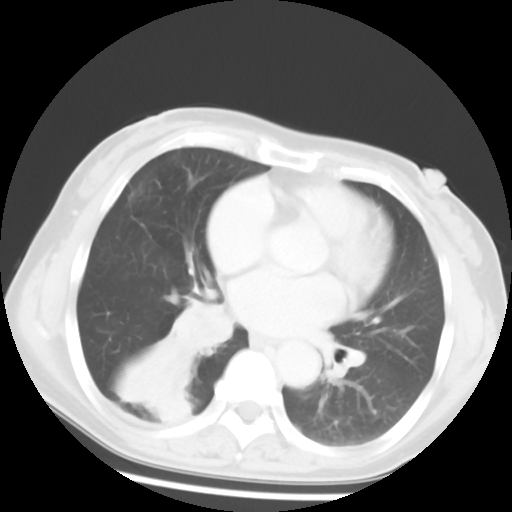
Chest CT, one axial slice; position 26 of 52 along the scan axis; reconstruction kernel STANDARD; 120 kVp; lung window (W 1500 / L -600 HU); 5 mm slice thickness; 512 × 512 image matrix, field of view 297 × 297 mm. Female patient, age 54 years. Case-level facts recorded for this patient, not image findings: clinical TNM (as recorded): T1c N0 M0; histopathological grade: G1-2.
Structures marked on this image (rectangle marked by the reading radiologist):
- lung tumour (recorded histology: squamous cell carcinoma): bounding box <175,293,252,381> (left, top, right, bottom; pixels)